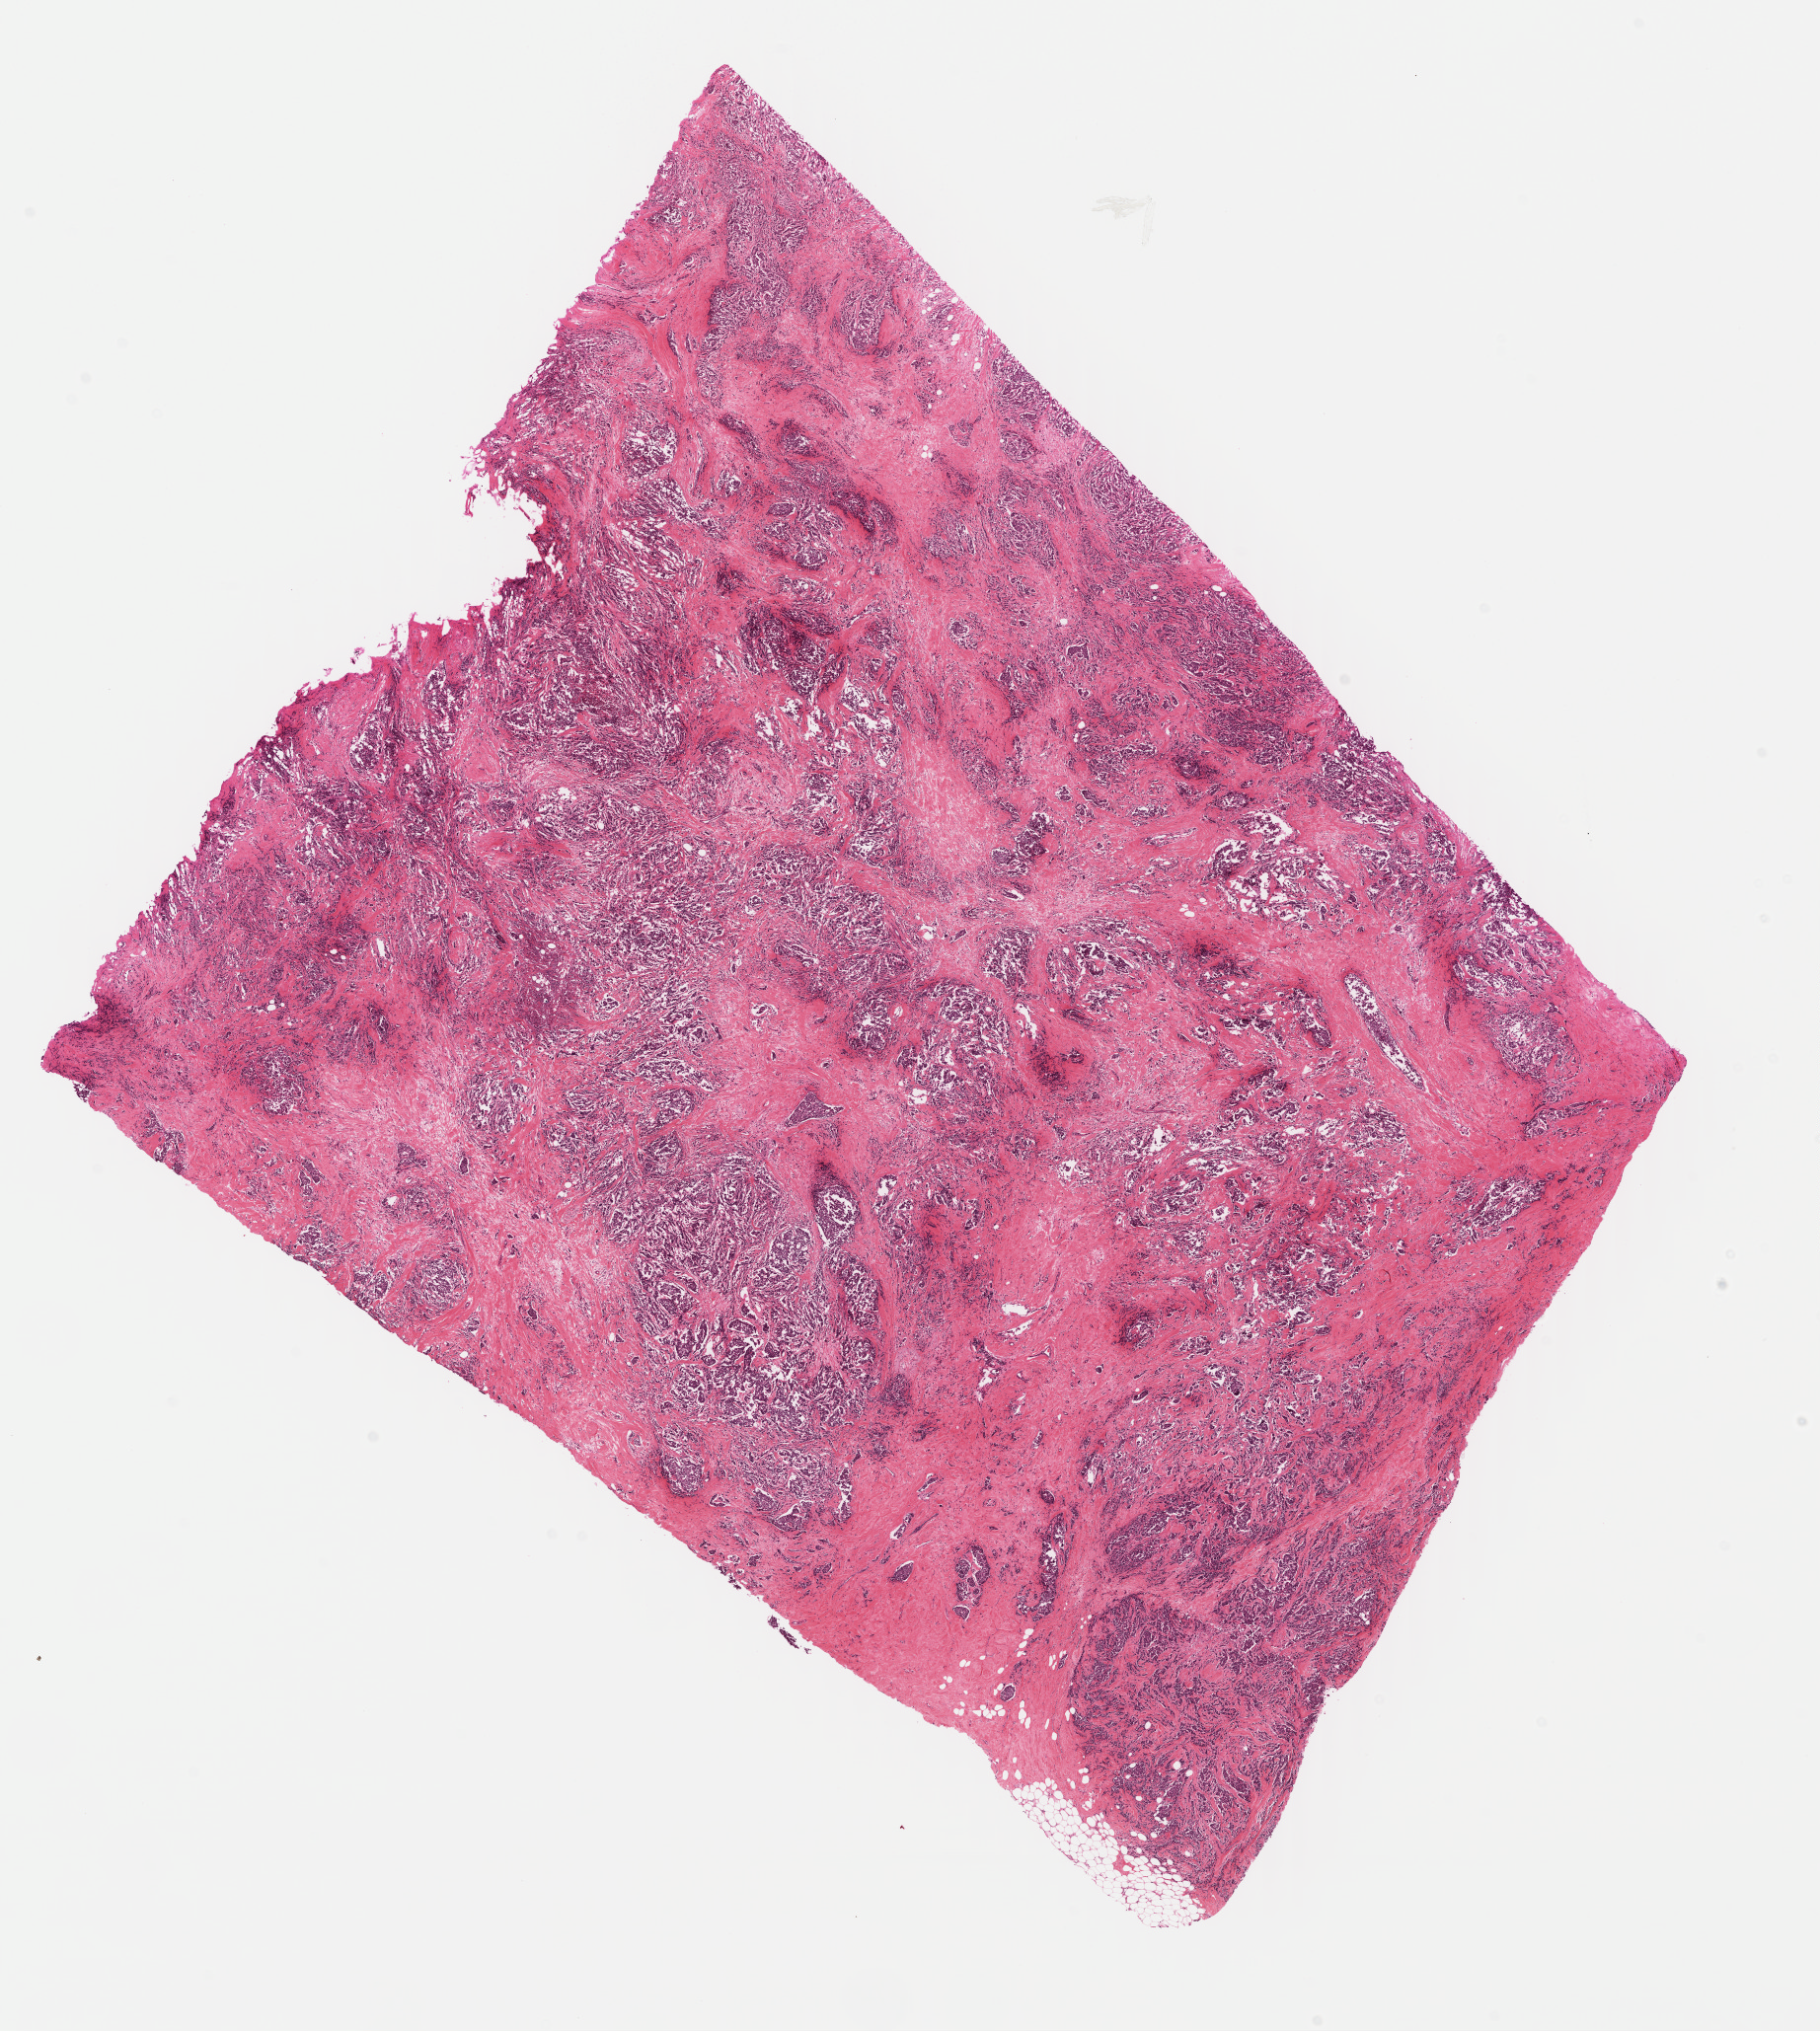
Hematoxylin and eosin (H&E) stained whole-slide image, shown as a low-resolution overview of the whole scanned area (about 14.5 x 16.2 mm, acquisition: 40x scan), FFPE section, primary tumour sample from the breast. Female, age 72 years at initial diagnosis.
Pathologic diagnosis: Lobular carcinoma, NOS. AJCC pathologic stage: IIIA. Lymph nodes positive (case pathology): 5 of 31 examined.